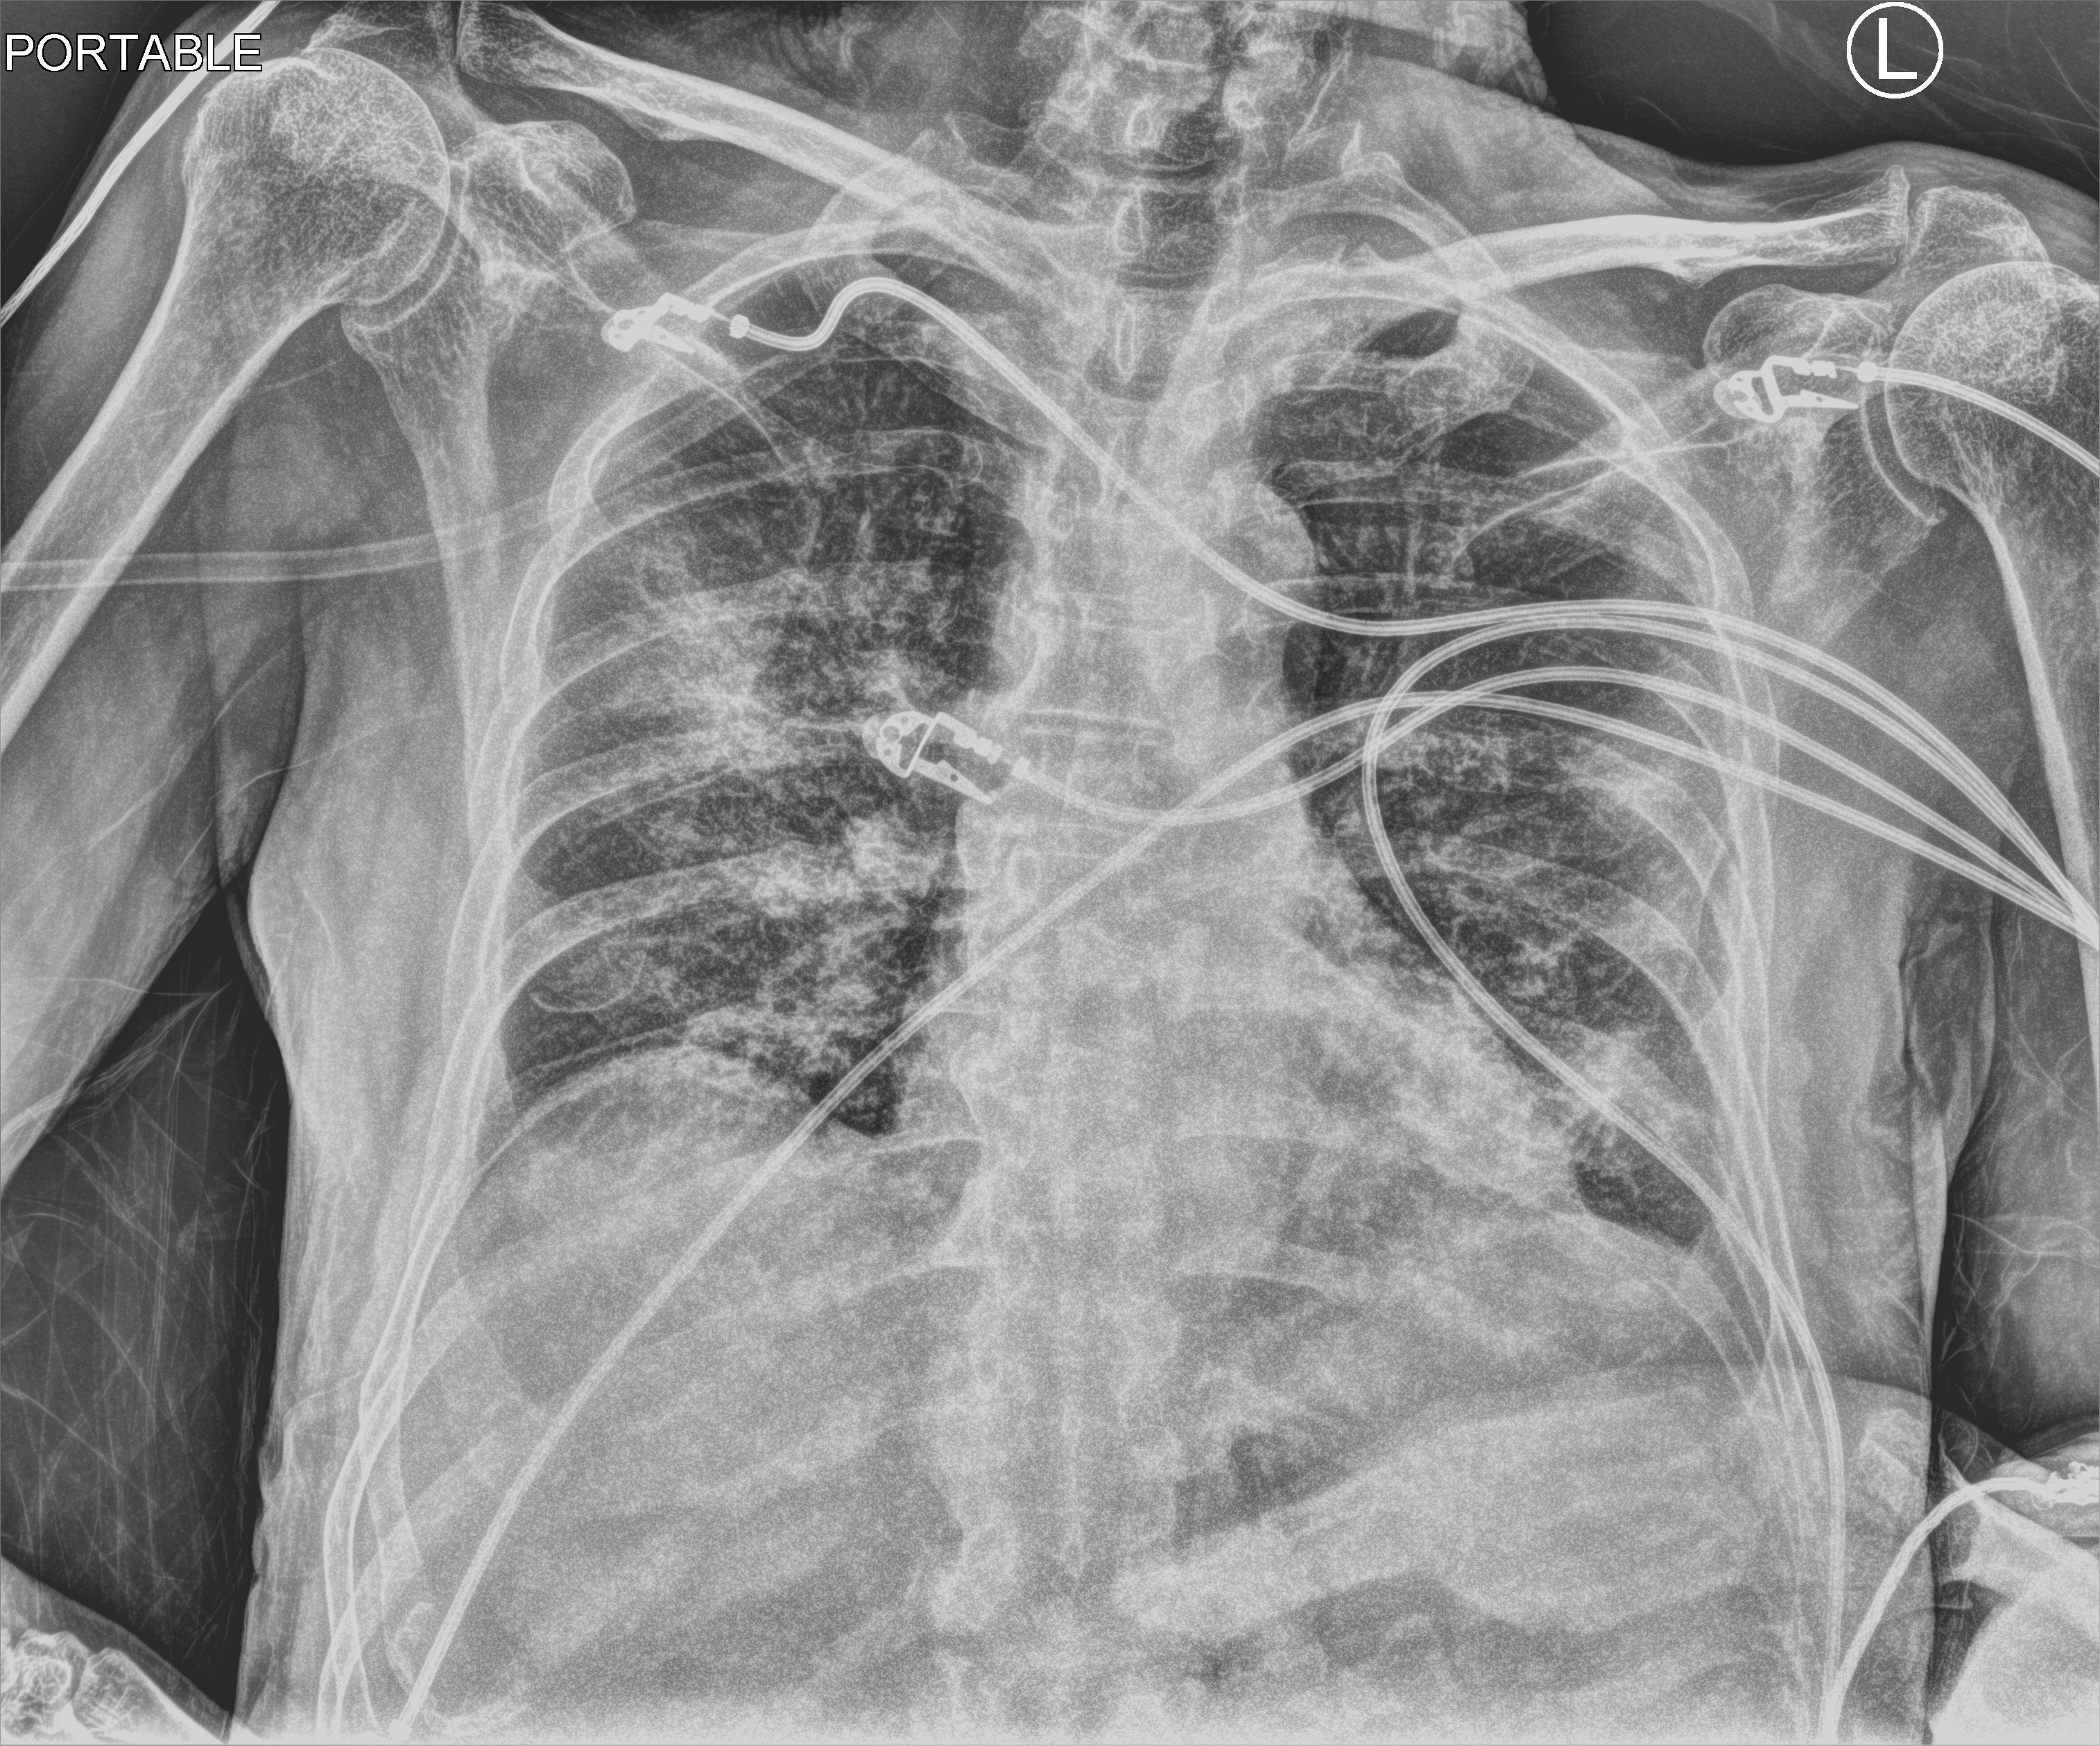
Bedside chest radiograph (computed radiography), anteroposterior (AP) projection. Patient hospitalised with COVID-19; male, aged 60–74 years.
Admission-level facts for this patient (not findings on this image; timing relative to this image not recorded):
- mechanically ventilated during this hospital stay: yes
- hypertension (admission record): yes